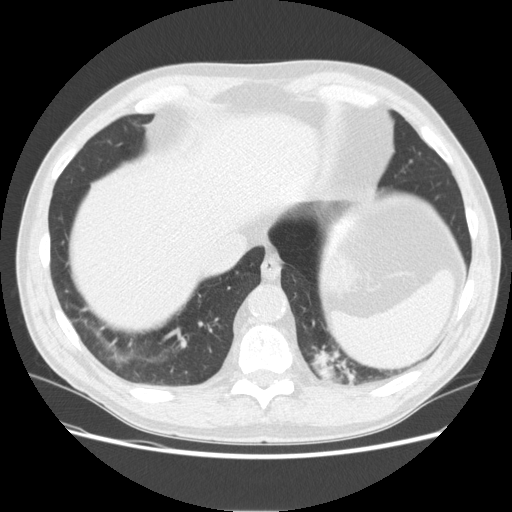
Low-dose screening chest CT, one axial slice. Slice 47 of 165 in the series (ordered by position). Lung window (W 1500 / L -600 HU). 512 × 512 image matrix, field of view 375 × 375 mm.
Annotated regions visible in this slice (expert manual segmentation):
- lesion 1 (tumor, upper lobe of left lung): box from (x=311, y=349) to (x=356, y=384) px